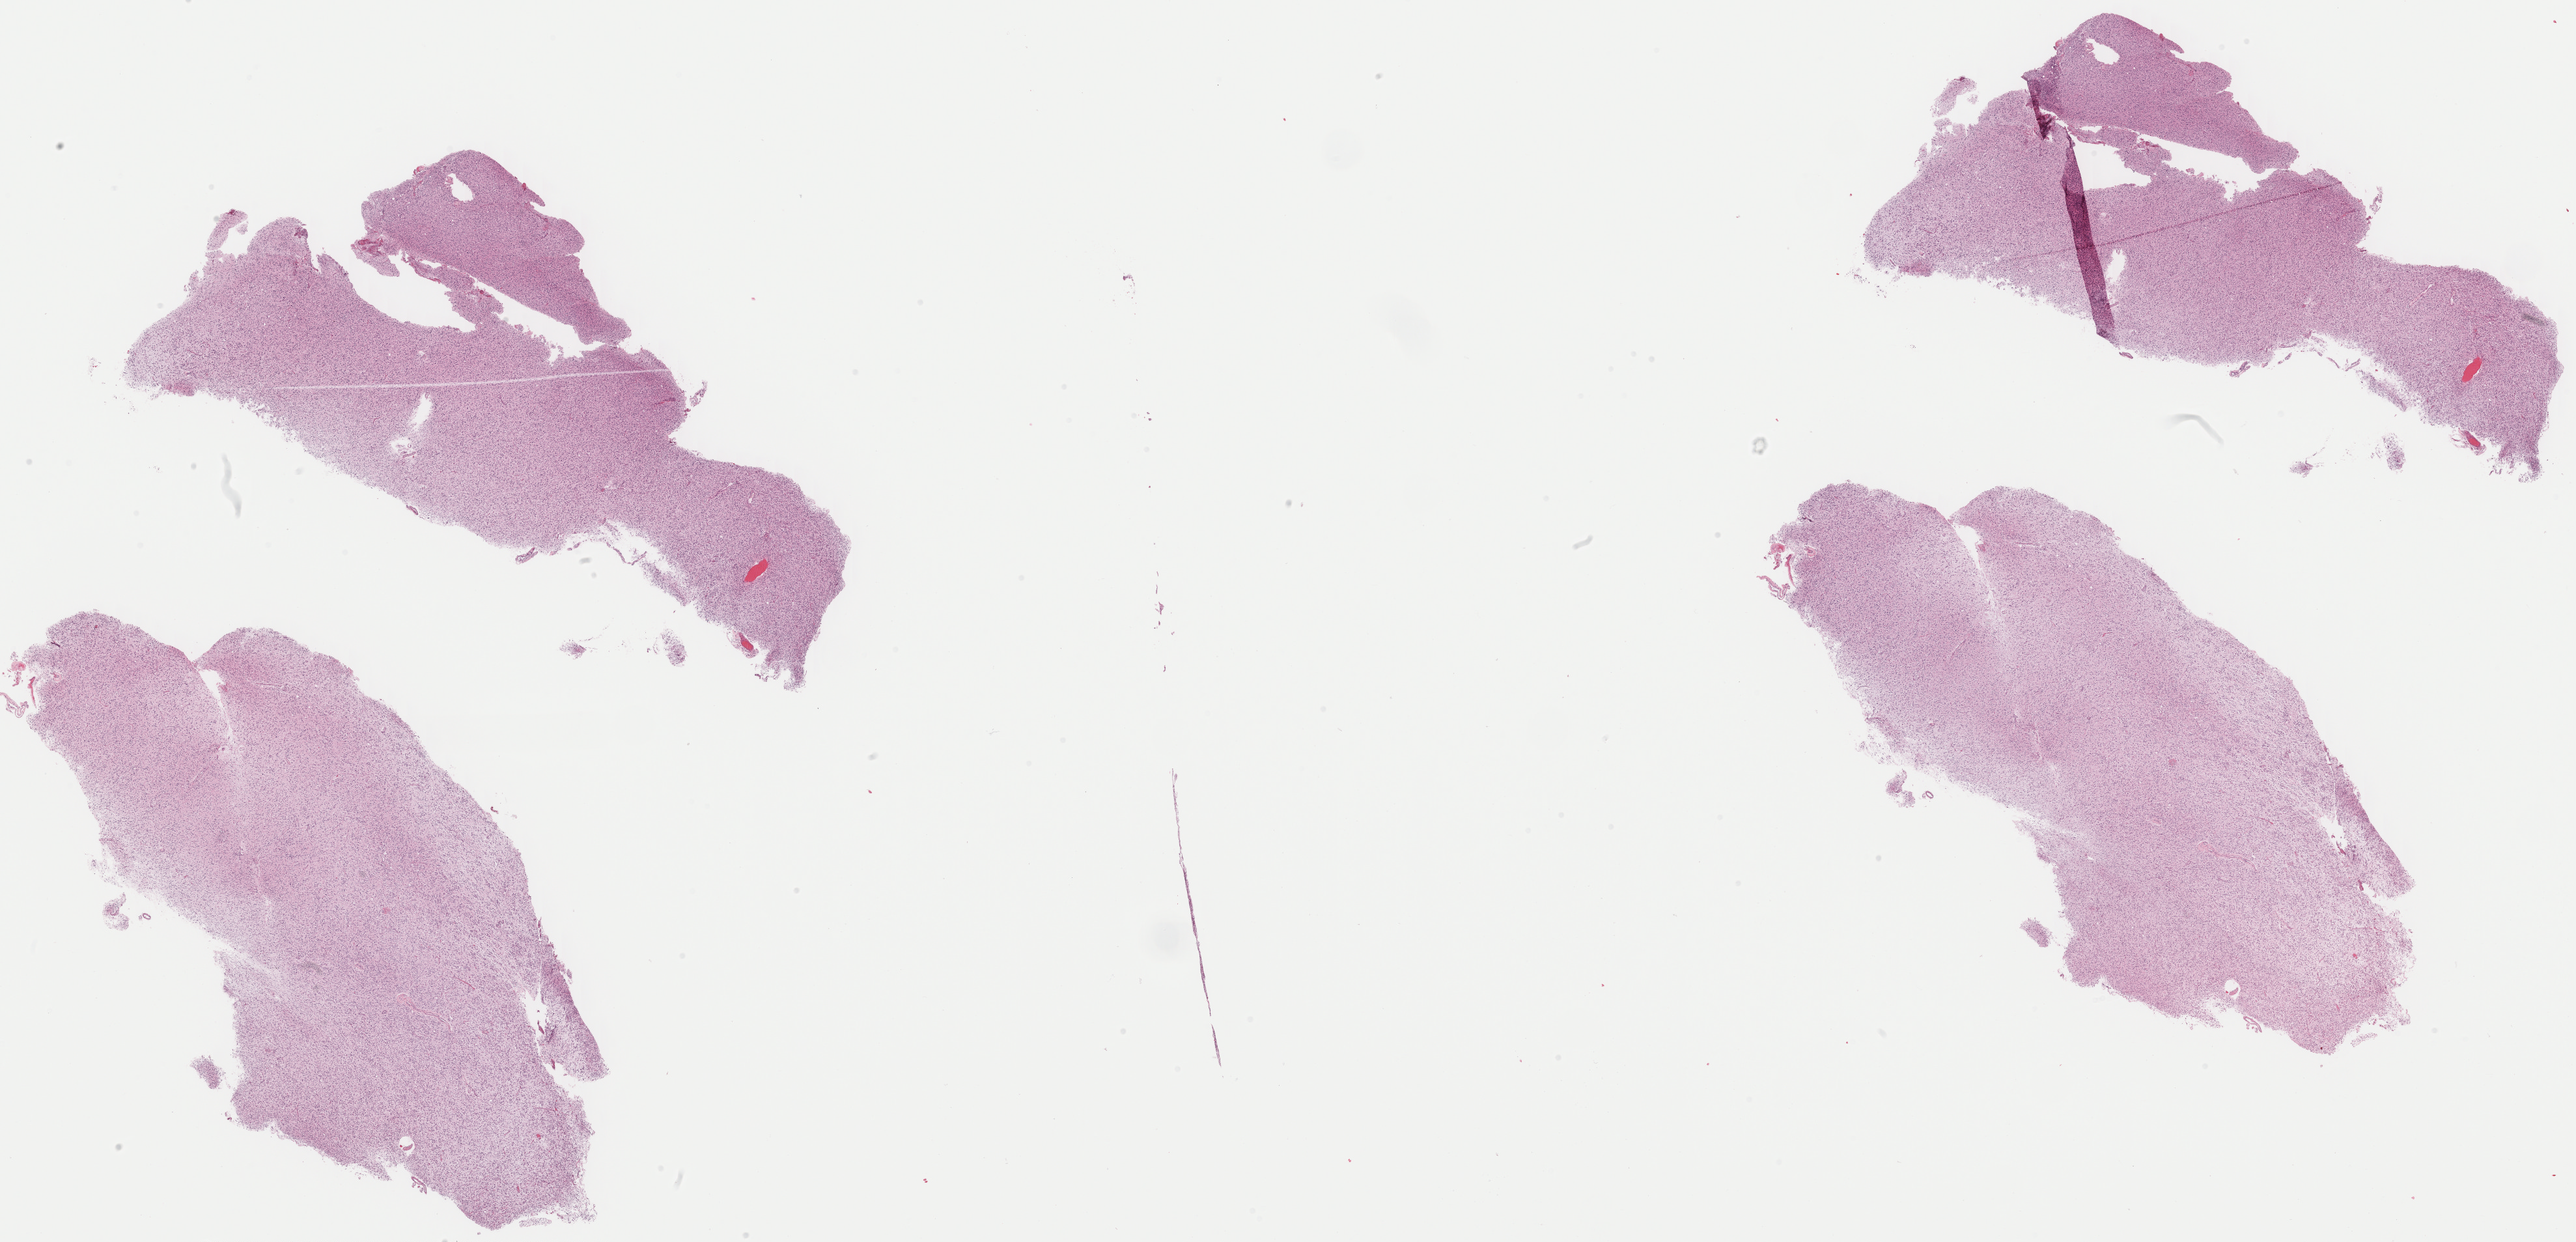
H&E whole-slide image — whole scanned area (about 31.2 x 15.0 mm, from a 40x scan) shown as a low-resolution overview. Formalin-fixed paraffin-embedded (FFPE) diagnostic section. Sample: primary tumour, brain. Patient: male, age at initial diagnosis 32 years. Histologic grade: G3 (poorly differentiated).
Histologic diagnosis: Astrocytoma, anaplastic (temporal lobe).